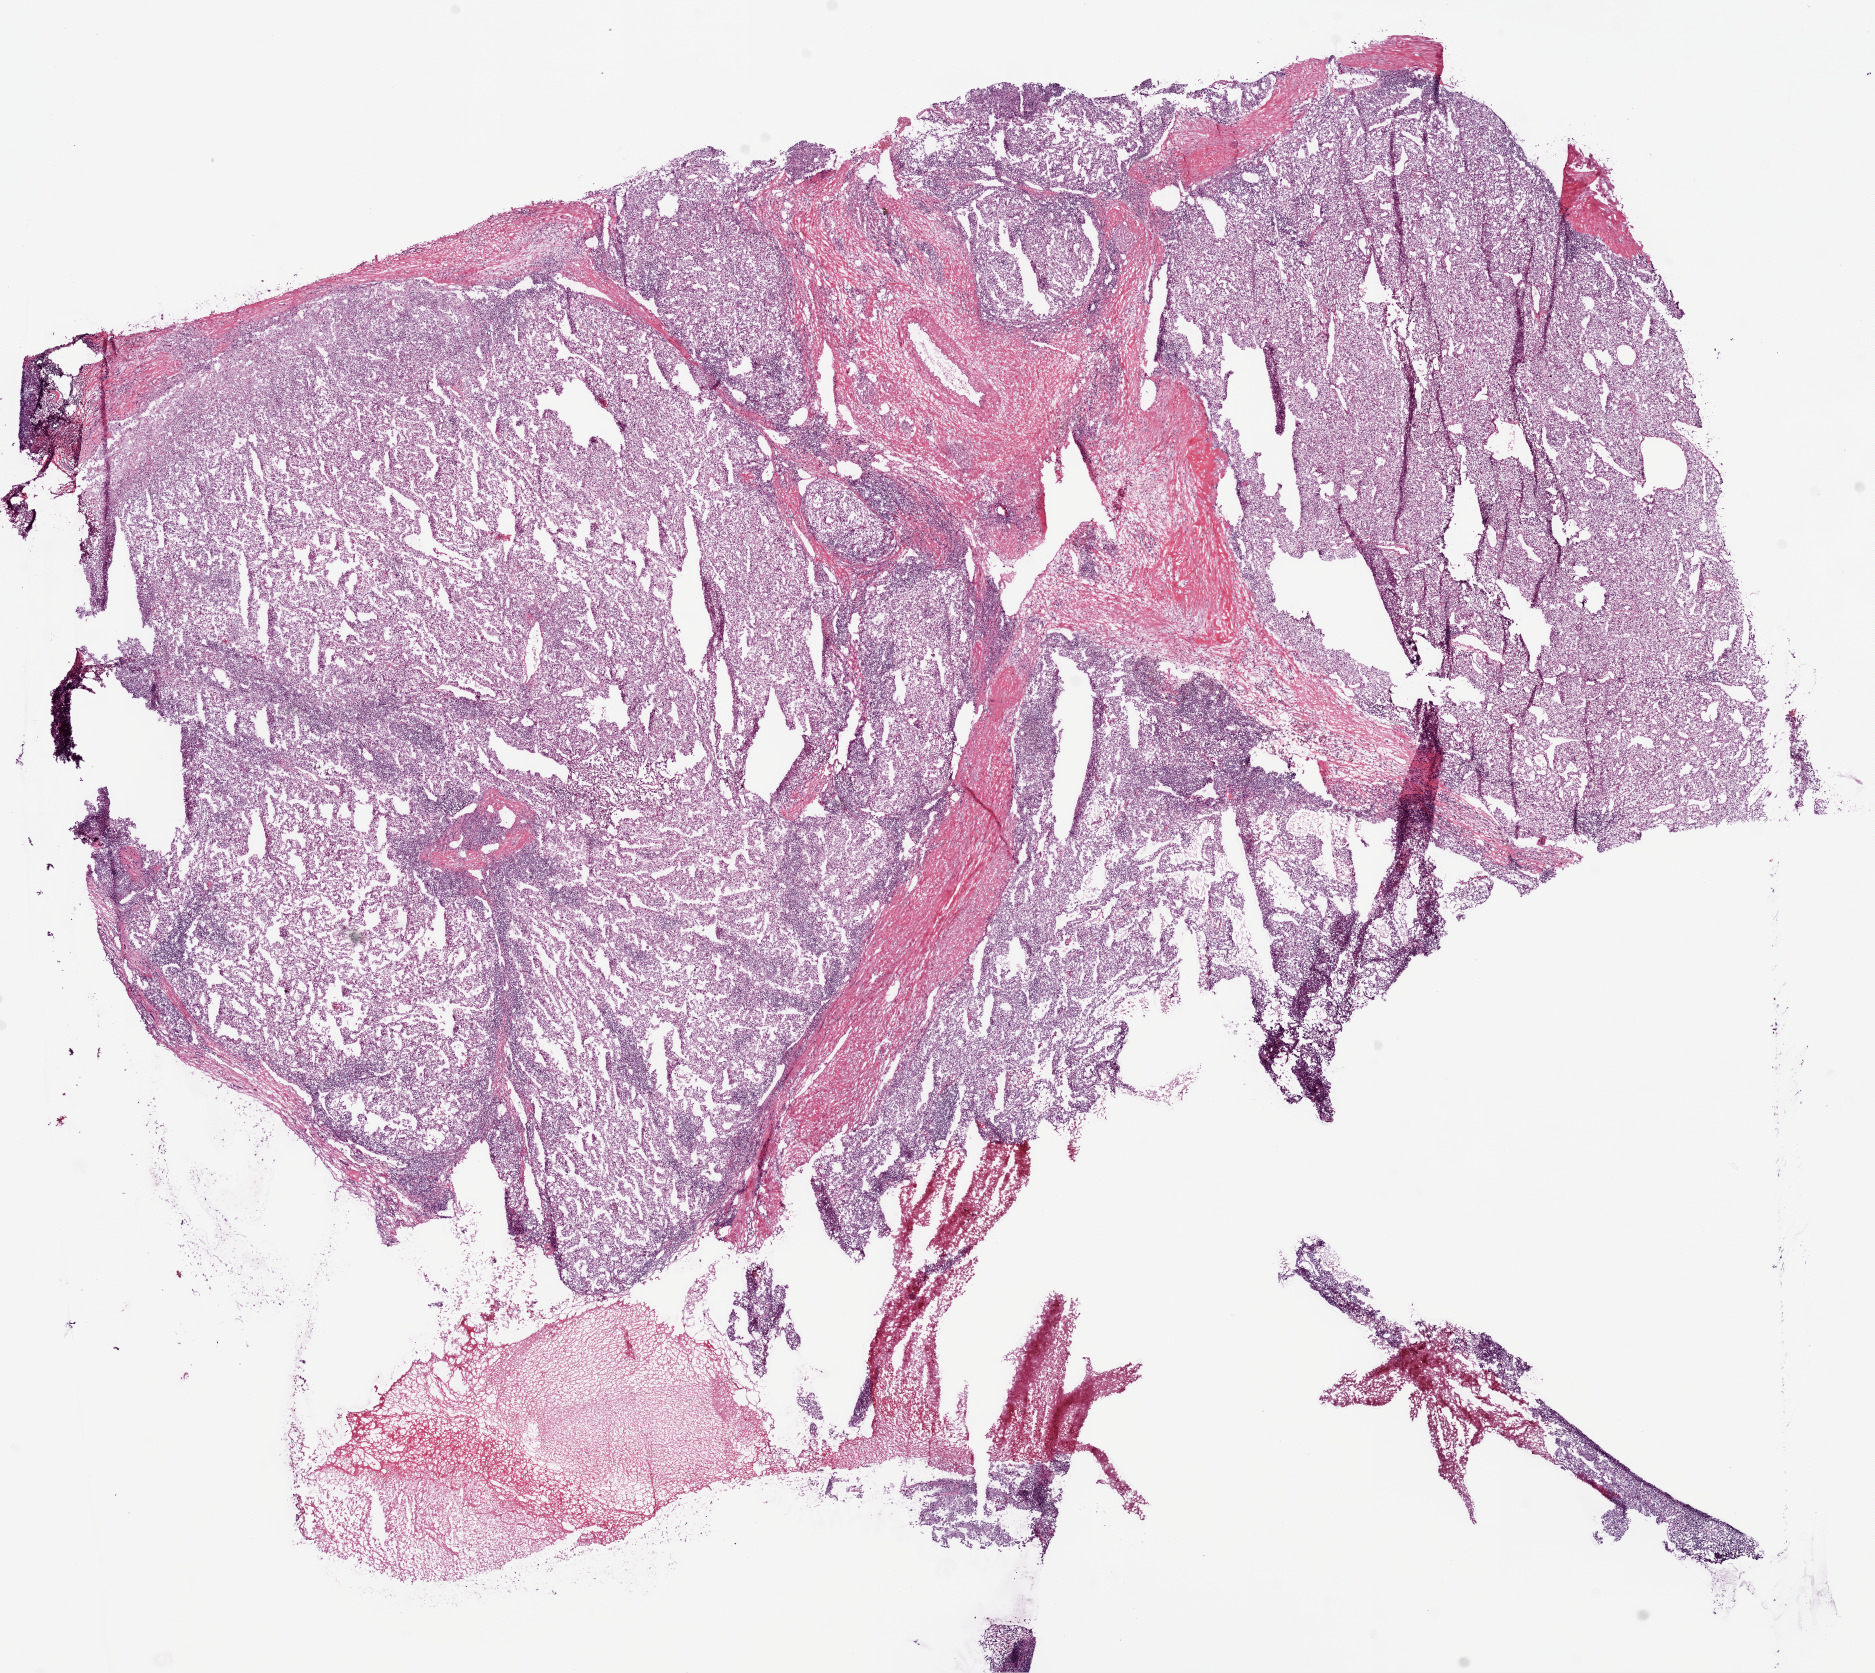
H&E-stained whole-slide image — low-resolution overview of the scanned area, about 15.0 x 13.4 mm; frozen section; primary tumour sample from the kidney. Male patient; age at initial diagnosis 65 years. Composition of this section per pathologist review: tumour cells 85%, tumour nuclei 85%.
Pathologic diagnosis: Clear cell adenocarcinoma, NOS.